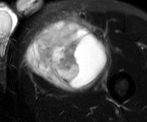
MRI of an extremity soft-tissue mass, one axial slice; position 41 of 52 along the scan axis; T2-weighted fat-saturated; MR volume resampled by the dataset authors to the PET/CT grid (not the native acquisition matrix); 3.27 mm slice thickness; 147 × 122 image matrix, field of view 144 × 119 mm. Male patient. From the clinical record (not read from this slice): histological type: pleiomorphic liposarcoma; grade: high; site of the primary tumour: left thigh.
Outlined on this slice (expert contour drawn on MRI and transferred to this co-registered scan by the dataset authors):
- gross tumour volume including surrounding oedema: box from (x=28, y=18) to (x=108, y=86) px
- gross tumour volume (mass): (x=28, y=23)–(x=104, y=86)